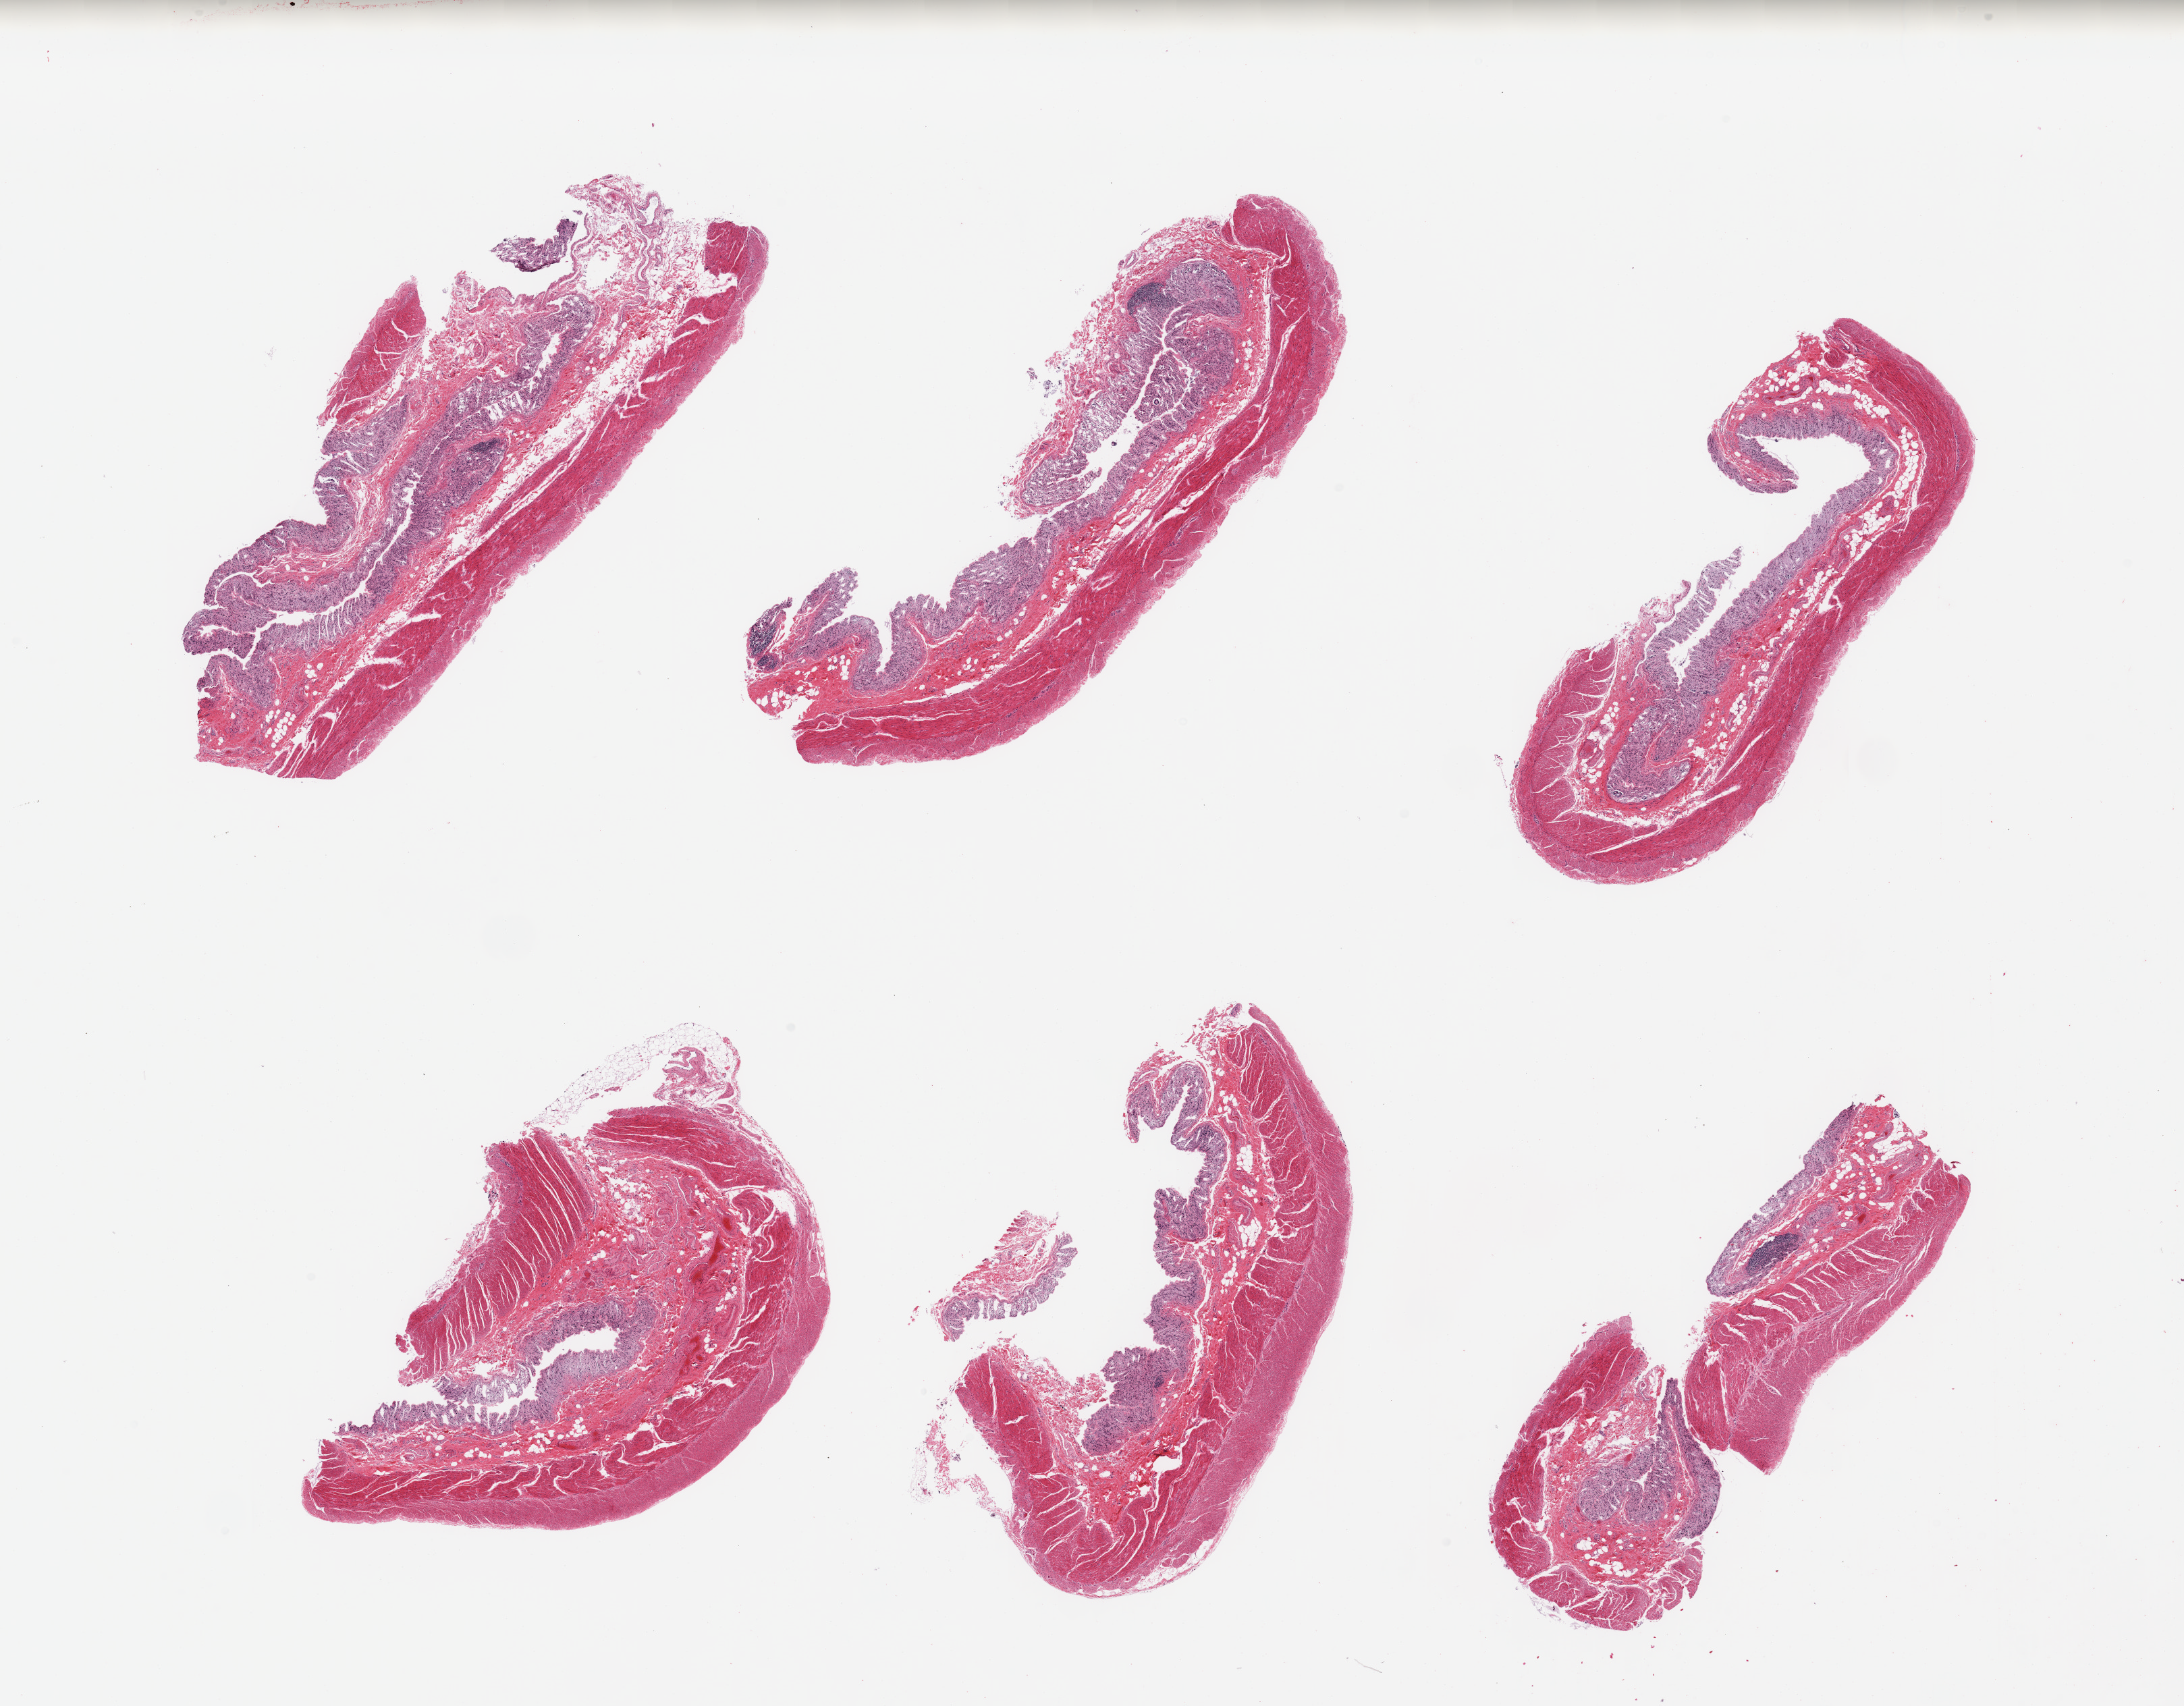
Haematoxylin and eosin whole-slide image — low-resolution overview of the scanned area, about 25.6 x 20.0 mm (slide scanned at 20x), PAXgene-fixed paraffin-embedded (PFPE) section, section of transverse colon (target tissue), tissue donor sample. Female donor.
• review note (as recorded): 6 pieces, target mucosa up to ~0.4mm, complete glandular mucosal autolysis, remnant lamina propria intact